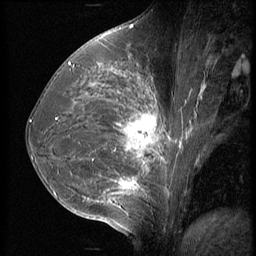
Breast MRI (dynamic contrast-enhanced), one sagittal slice; position 29 of 56 along the scan axis; 3 images stored at this slice position (order not interpretable as contrast timing); 1.5 T; TE 4.2 ms, TR 9 ms; 2.5 mm slice thickness; 256 × 256 image matrix, field of view 180 × 180 mm. Female patient, age 35 years. Case-level facts recorded for this patient, not image findings: setting: breast cancer imaged before/during neoadjuvant chemotherapy; receptor status: HR-positive, HER2-negative.
Annotated regions visible in this slice (semi-automatic segmentation, software-assisted and operator-edited):
- analysis volume of interest (the breast-tissue region the enhancement analysis was run in; not a lesion): bounding box [x1, y1, x2, y2] px = [63, 60, 190, 218]
- tumour enhancement mask (voxels above the 140 % enhancement threshold inside the analysis volume of interest): [69, 64, 169, 194]